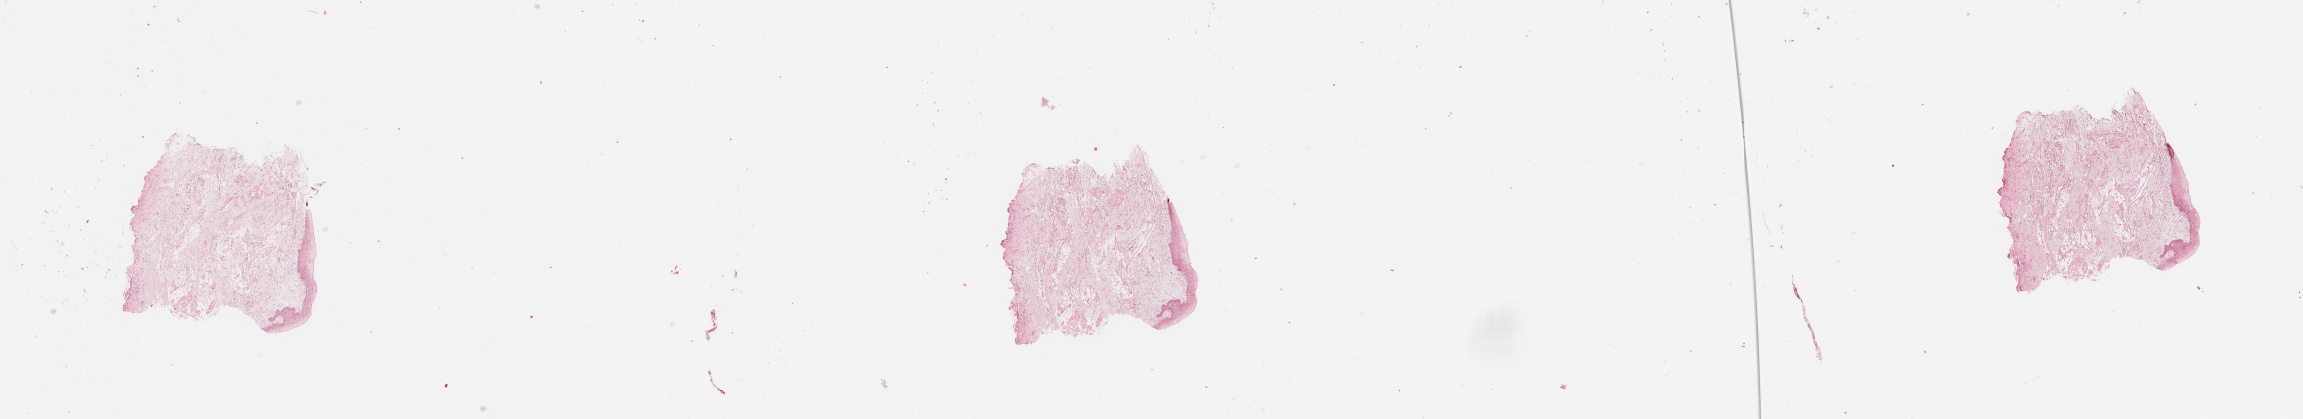
H&E whole-slide image, shown as a low-resolution overview of the whole scanned area (about 36.4 x 6.6 mm, acquisition: 20x scan); head and neck, normal (non-tumour) tissue. Male, 59 y/o.
This section: normal (non-tumour) tissue from the same patient. Patient diagnosis: Squamous cell carcinoma, NOS (tongue, NOS).